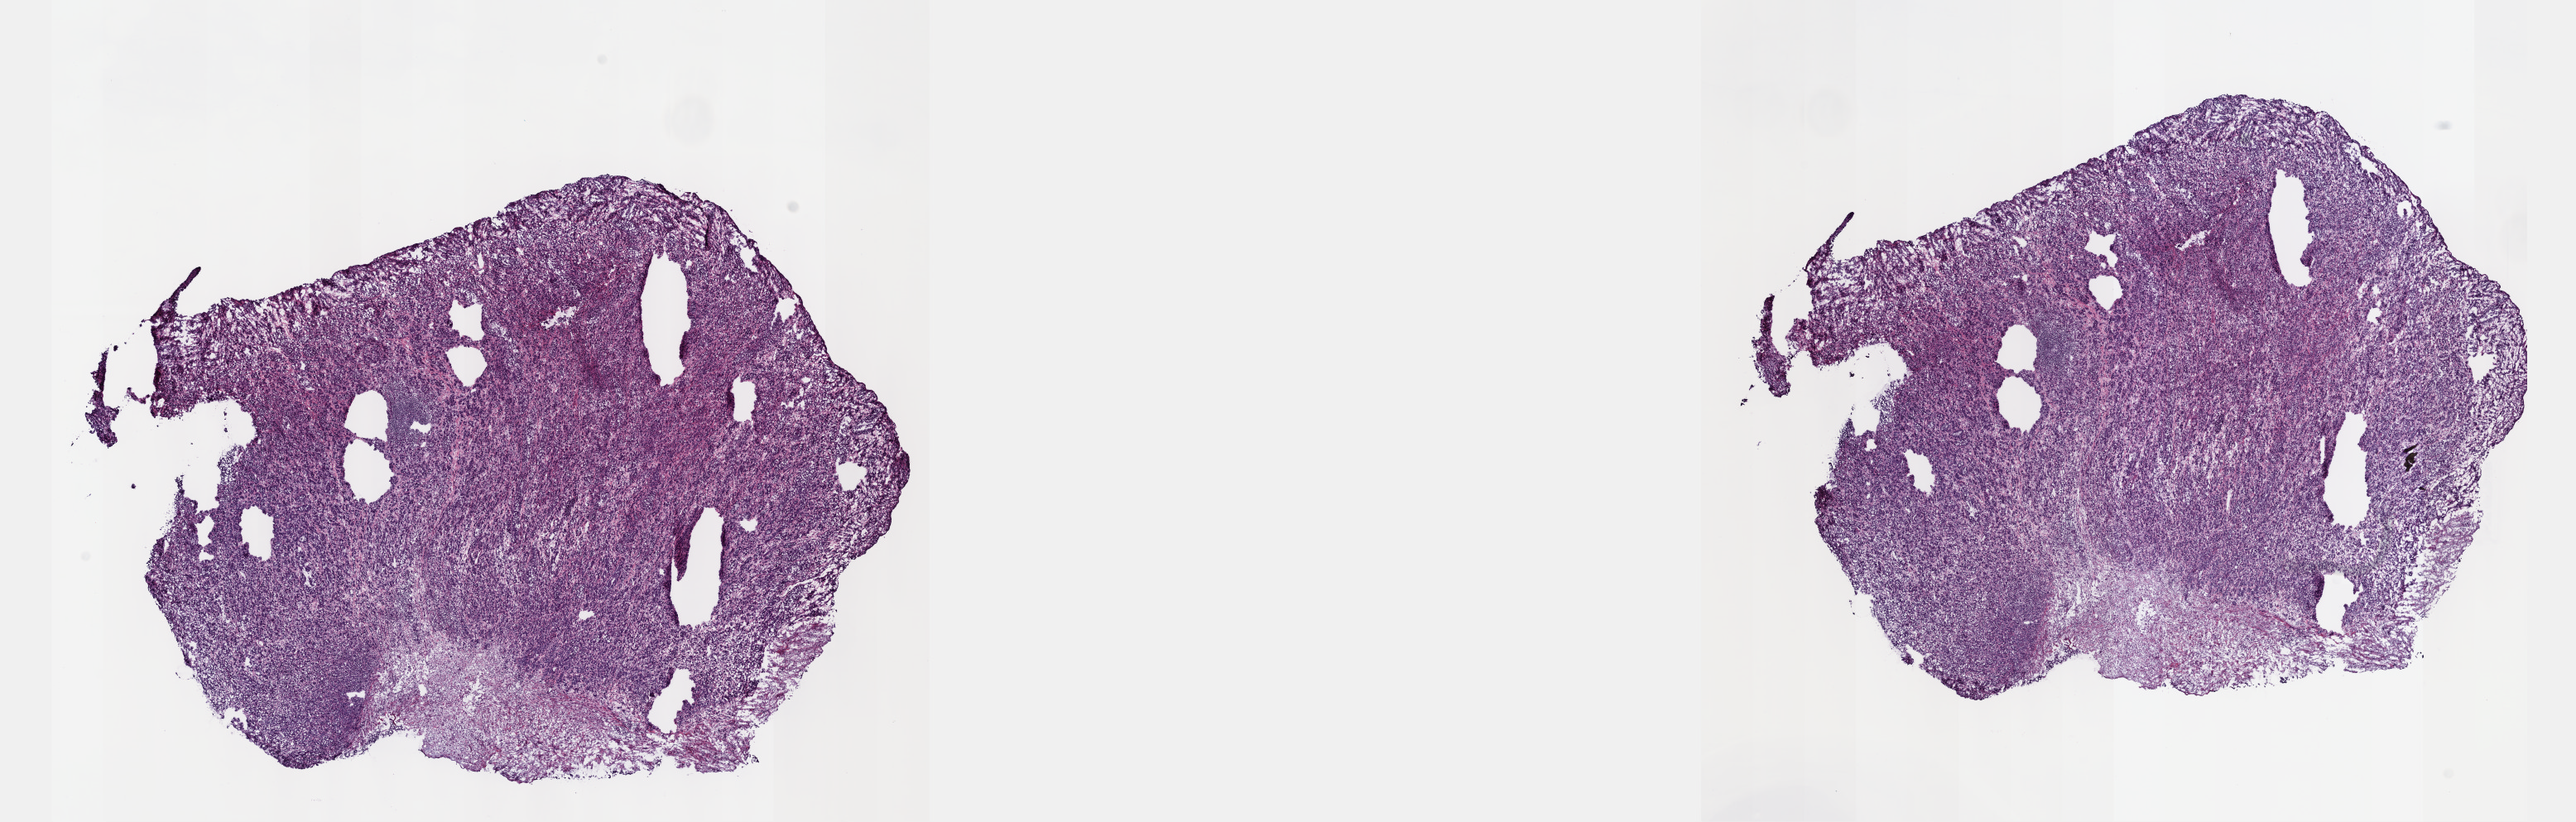
Digitized Hematoxylin and eosin (H&E) stained tissue section (whole slide) — shown as a low-resolution overview of the whole scanned area (about 25.1 x 8.0 mm), frozen section from the top of the tissue portion, metastatic tumour sample, sampled site not recorded. Female patient.
This section: metastatic tumour tissue. Patient diagnosis: Malignant melanoma, NOS.